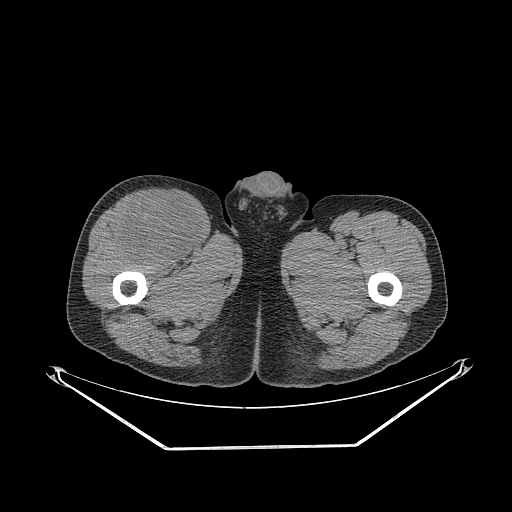
CT of an extremity soft-tissue mass (from a PET/CT study), one axial slice. Position 294 of 311 along the scan axis. 140 kVp. Soft-tissue window (W 400 / L 40 HU). 512 × 512 image matrix, field of view 500 × 500 mm. Male patient. From the clinical record (not read from this slice): histological type: pleiomorphic leiomyosarcoma; grade: intermediate; site of the primary tumour: right thigh.
Outlined on this slice (expert contour drawn on MRI and transferred to this co-registered scan by the dataset authors):
- gross tumour volume including surrounding oedema: box from (x=119, y=192) to (x=204, y=264) px
- gross tumour volume (mass): (x=119, y=192)–(x=204, y=264)